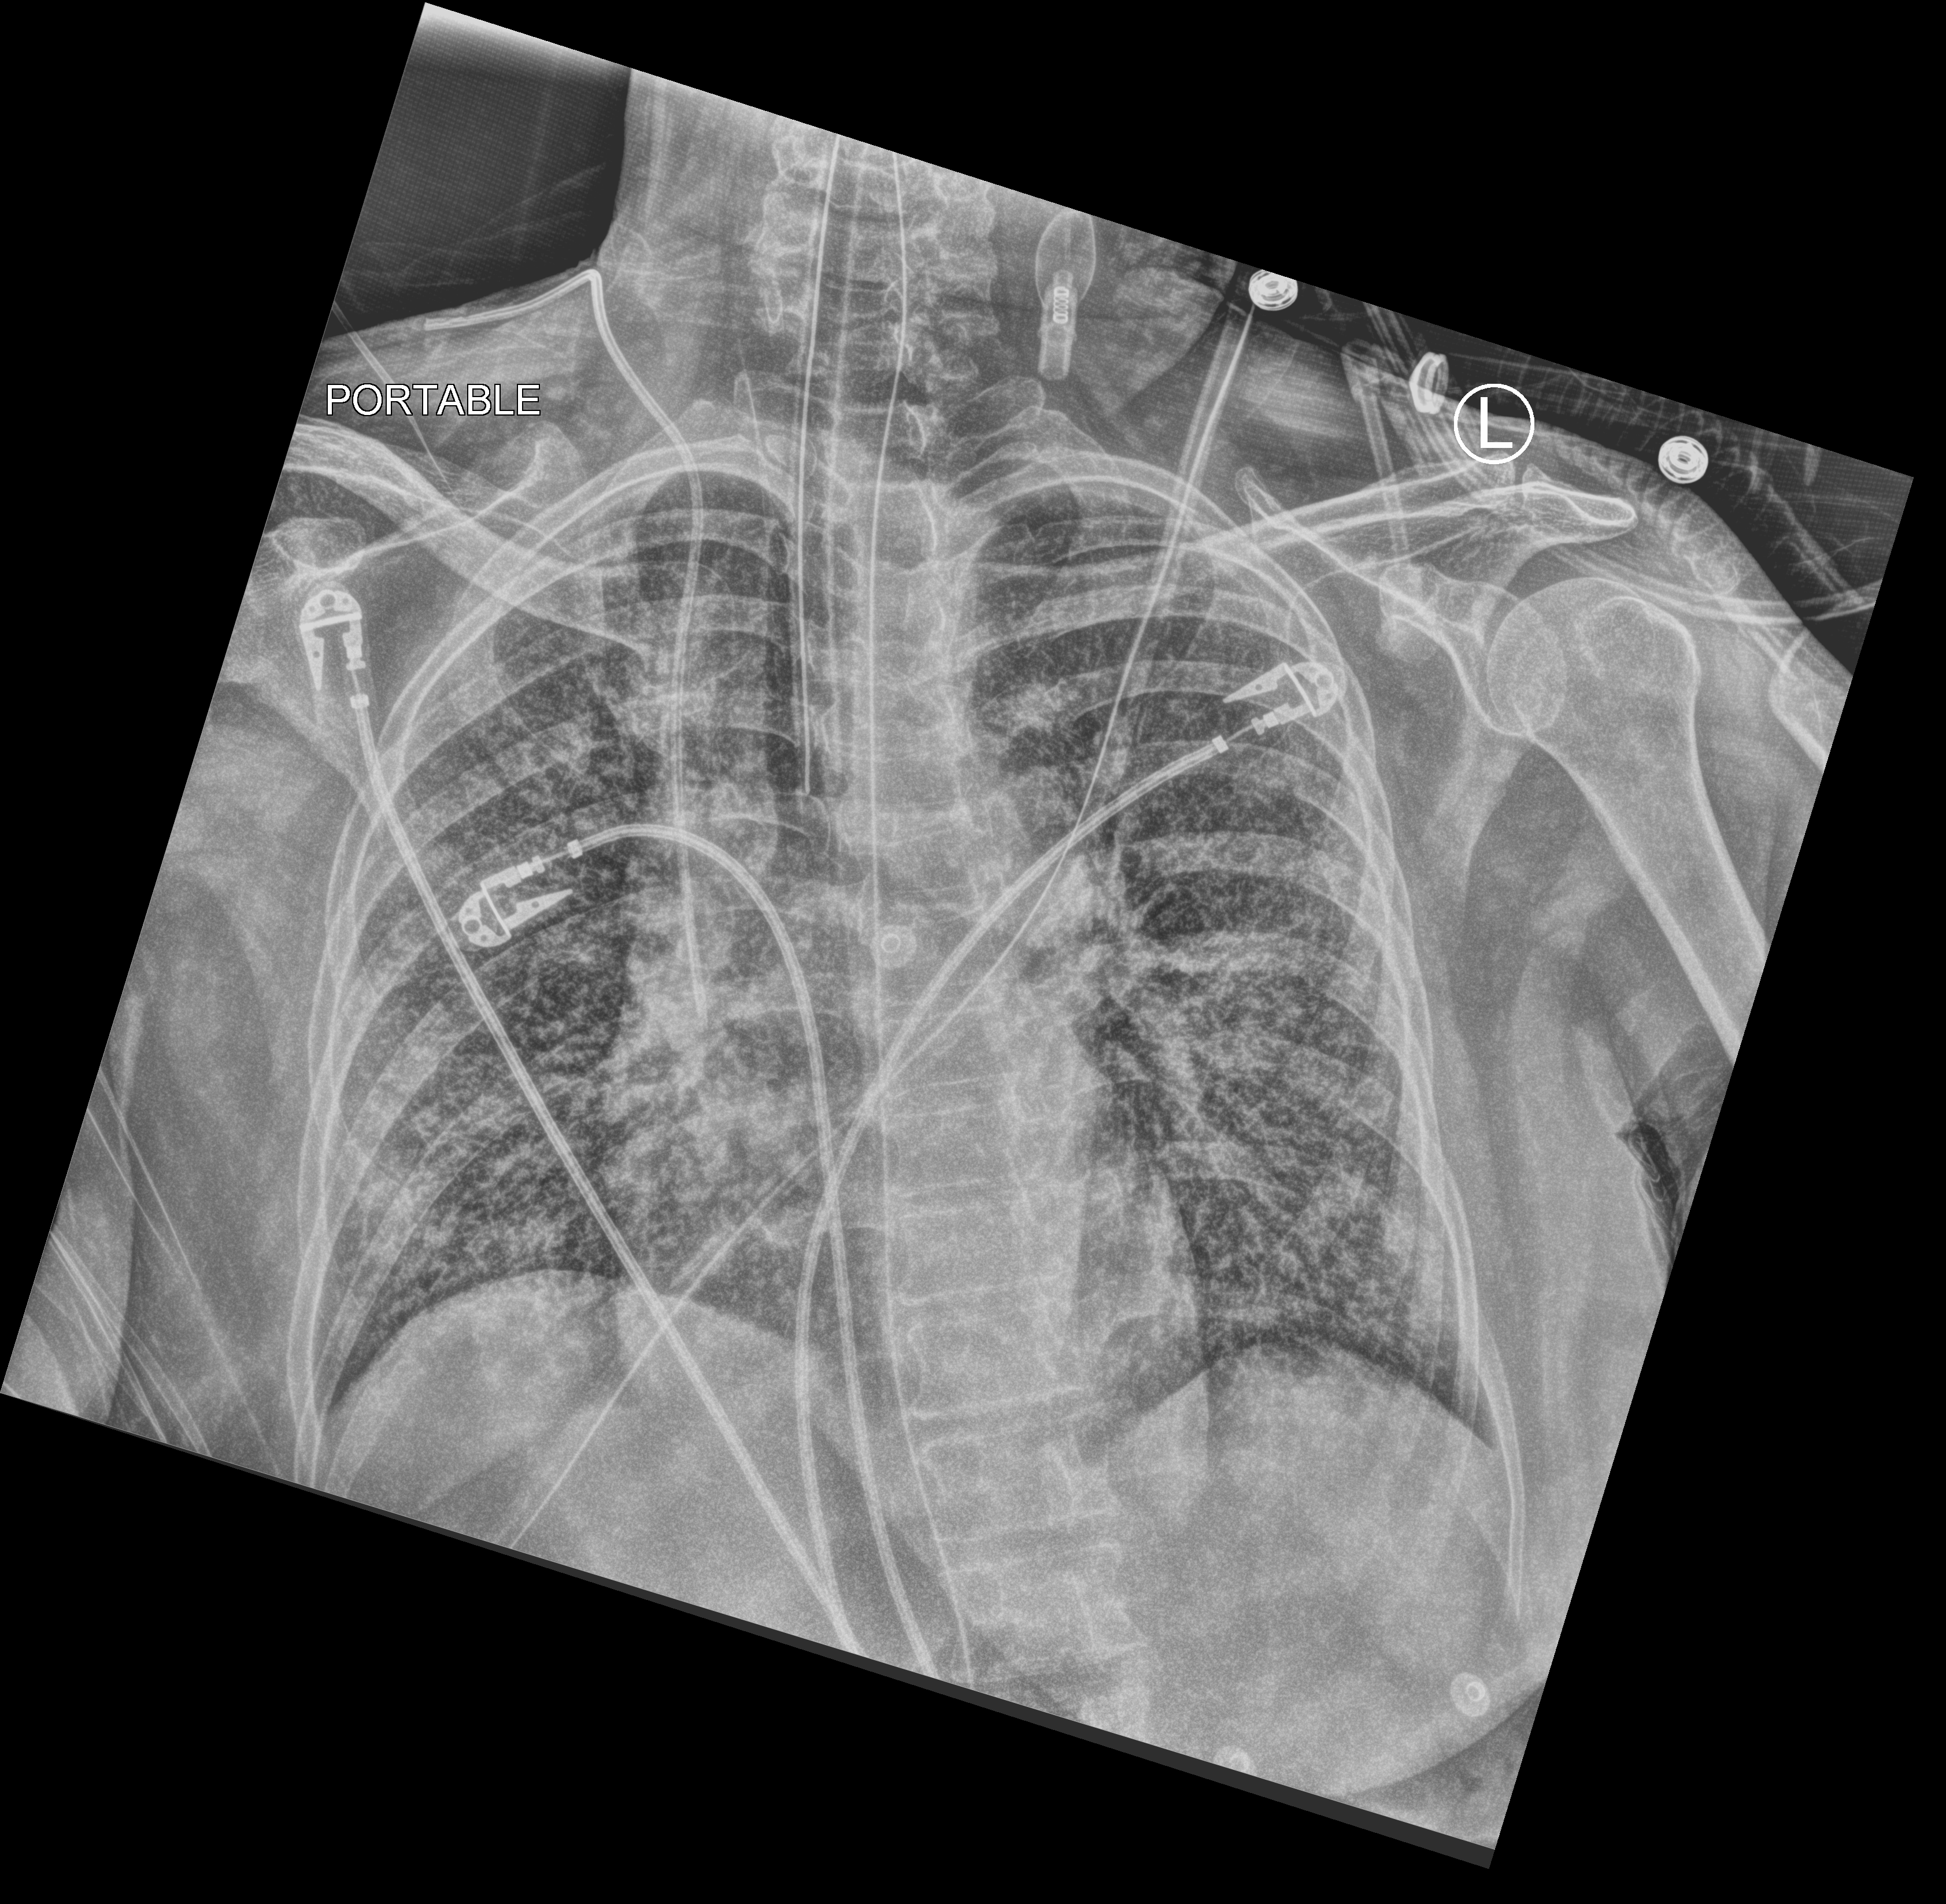
Portable chest radiograph, anteroposterior (AP) projection. Female patient hospitalised with COVID-19, age 60–74 years.
From the hospital-stay record, not from the radiograph (when in the stay this image was taken is not recorded): mechanically ventilated during this hospital stay: yes.